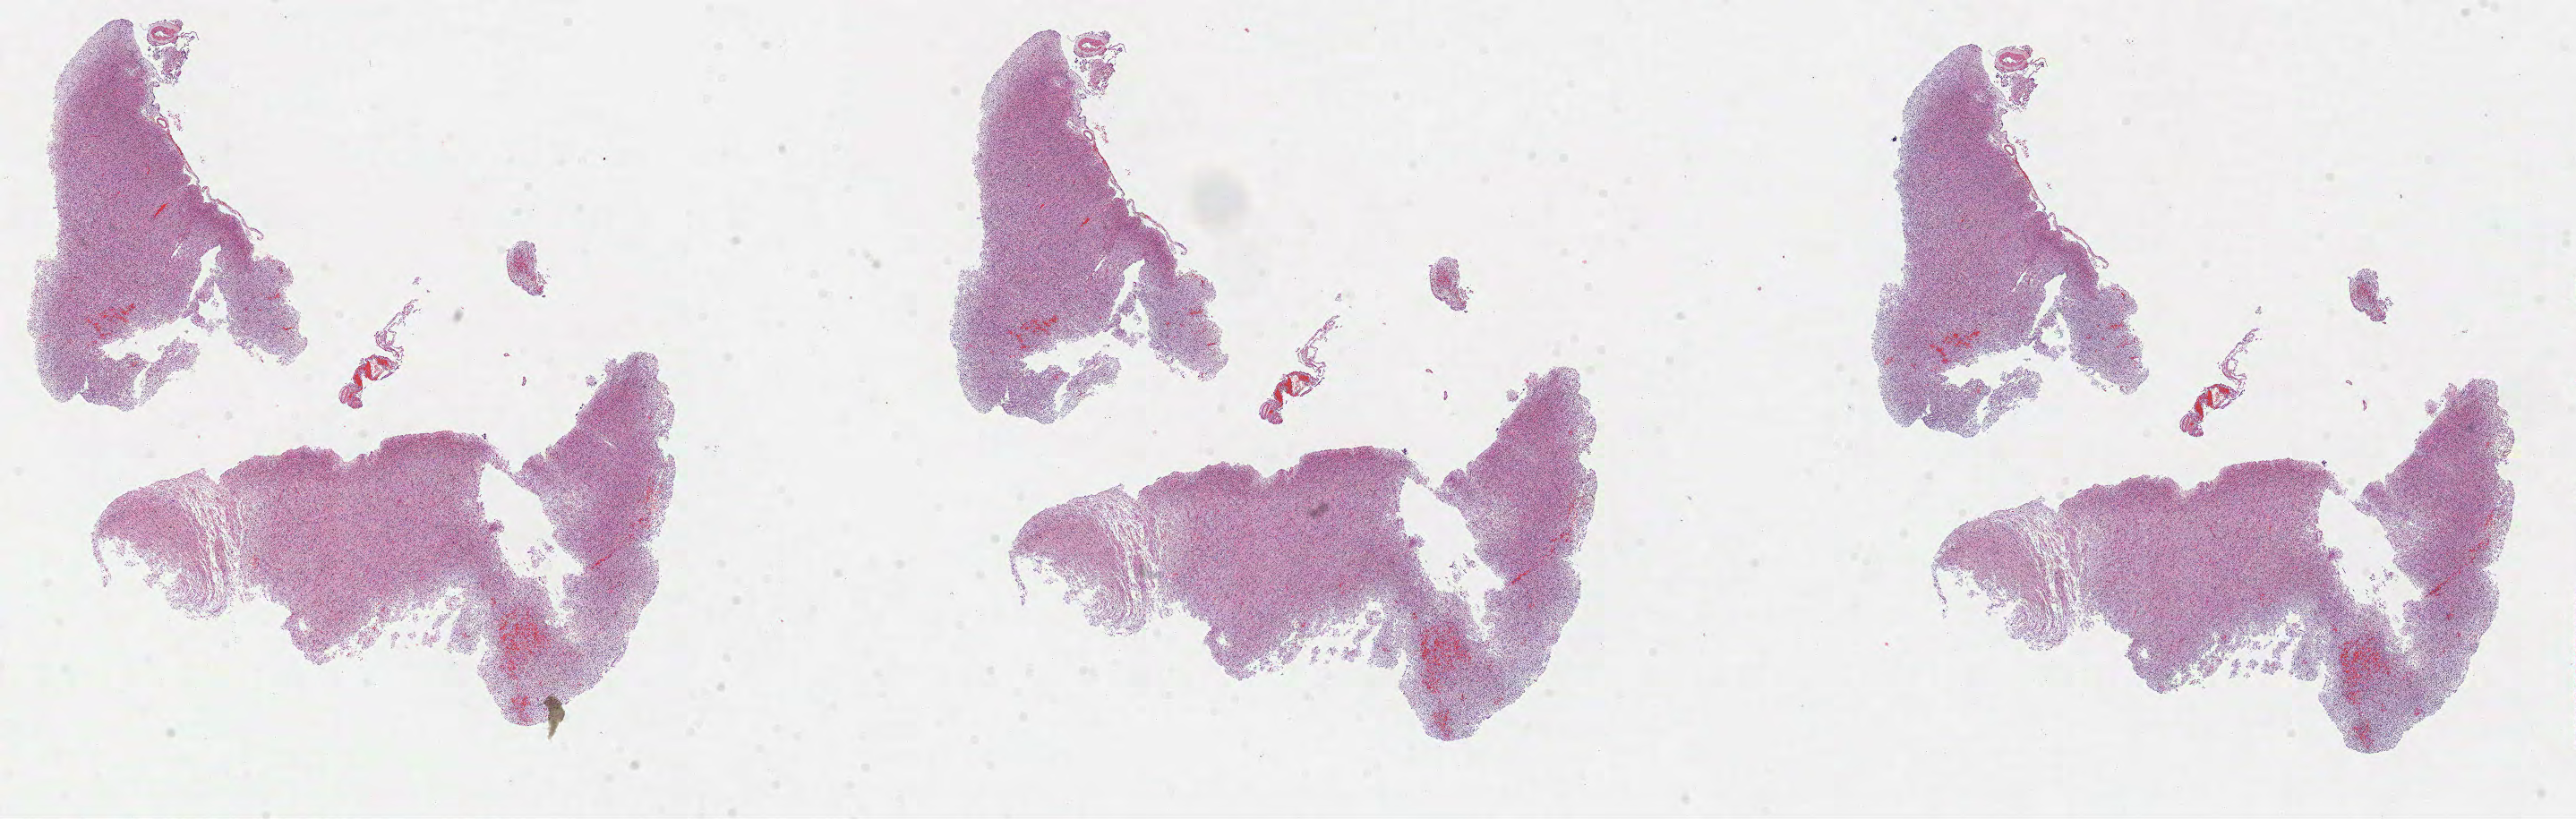
Whole-slide histology image, Hematoxylin and eosin (H&E) stained, whole scanned area (about 23.2 x 7.4 mm, slide scanned at 40x) shown as a low-resolution overview, formalin-fixed paraffin-embedded (FFPE) diagnostic section, primary tumour sample from the brain. Female, age 61 years at initial diagnosis. Histologic grade: G3 (poorly differentiated).
* histologic diagnosis: Mixed glioma